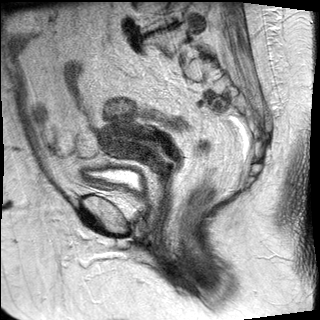
Pelvic MRI for cervical cancer, one sagittal slice; position 12 of 27 along the scan axis; T2-weighted; 1.5 T; TE 89 ms, TR 2740 ms; 4 mm slice thickness; 320 × 320 image matrix. Female patient, age 67 years.
Structures marked on this image (manually delineated by an expert):
- uterus and cervix: bounding box (x1, y1, x2, y2) in pixels: (96, 121, 183, 175)